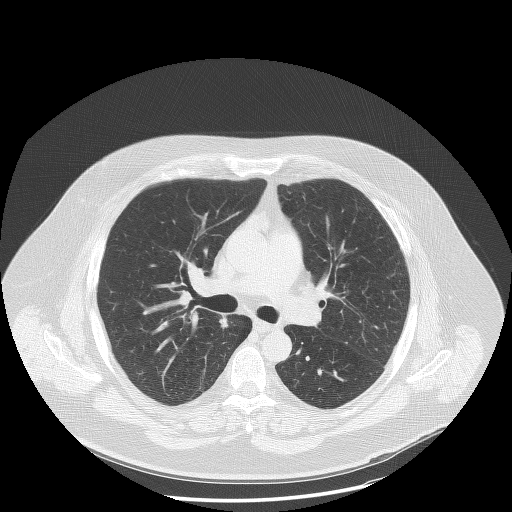
Axial slice from a low-dose chest CT screening exam. Second annual screen. Lung window (W 1500 / L -600 HU). Slice 49 of 132 in the series. Male participant, aged 58 years at enrolment. Former smoker at enrolment.
• Lesion marked by an expert reader, bounding box <202,304,243,345> (left, top, right, bottom; pixels).
• Screening reader's record for this exam: no non-calcified nodule ≥4 mm recorded.
• Participant outcome: lung cancer diagnosed 471 days after this screen — squamous cell carcinoma, NOS, right upper lobe, moderately differentiated (G2), stage IA (AJCC 6th edition), 18 mm at pathology.